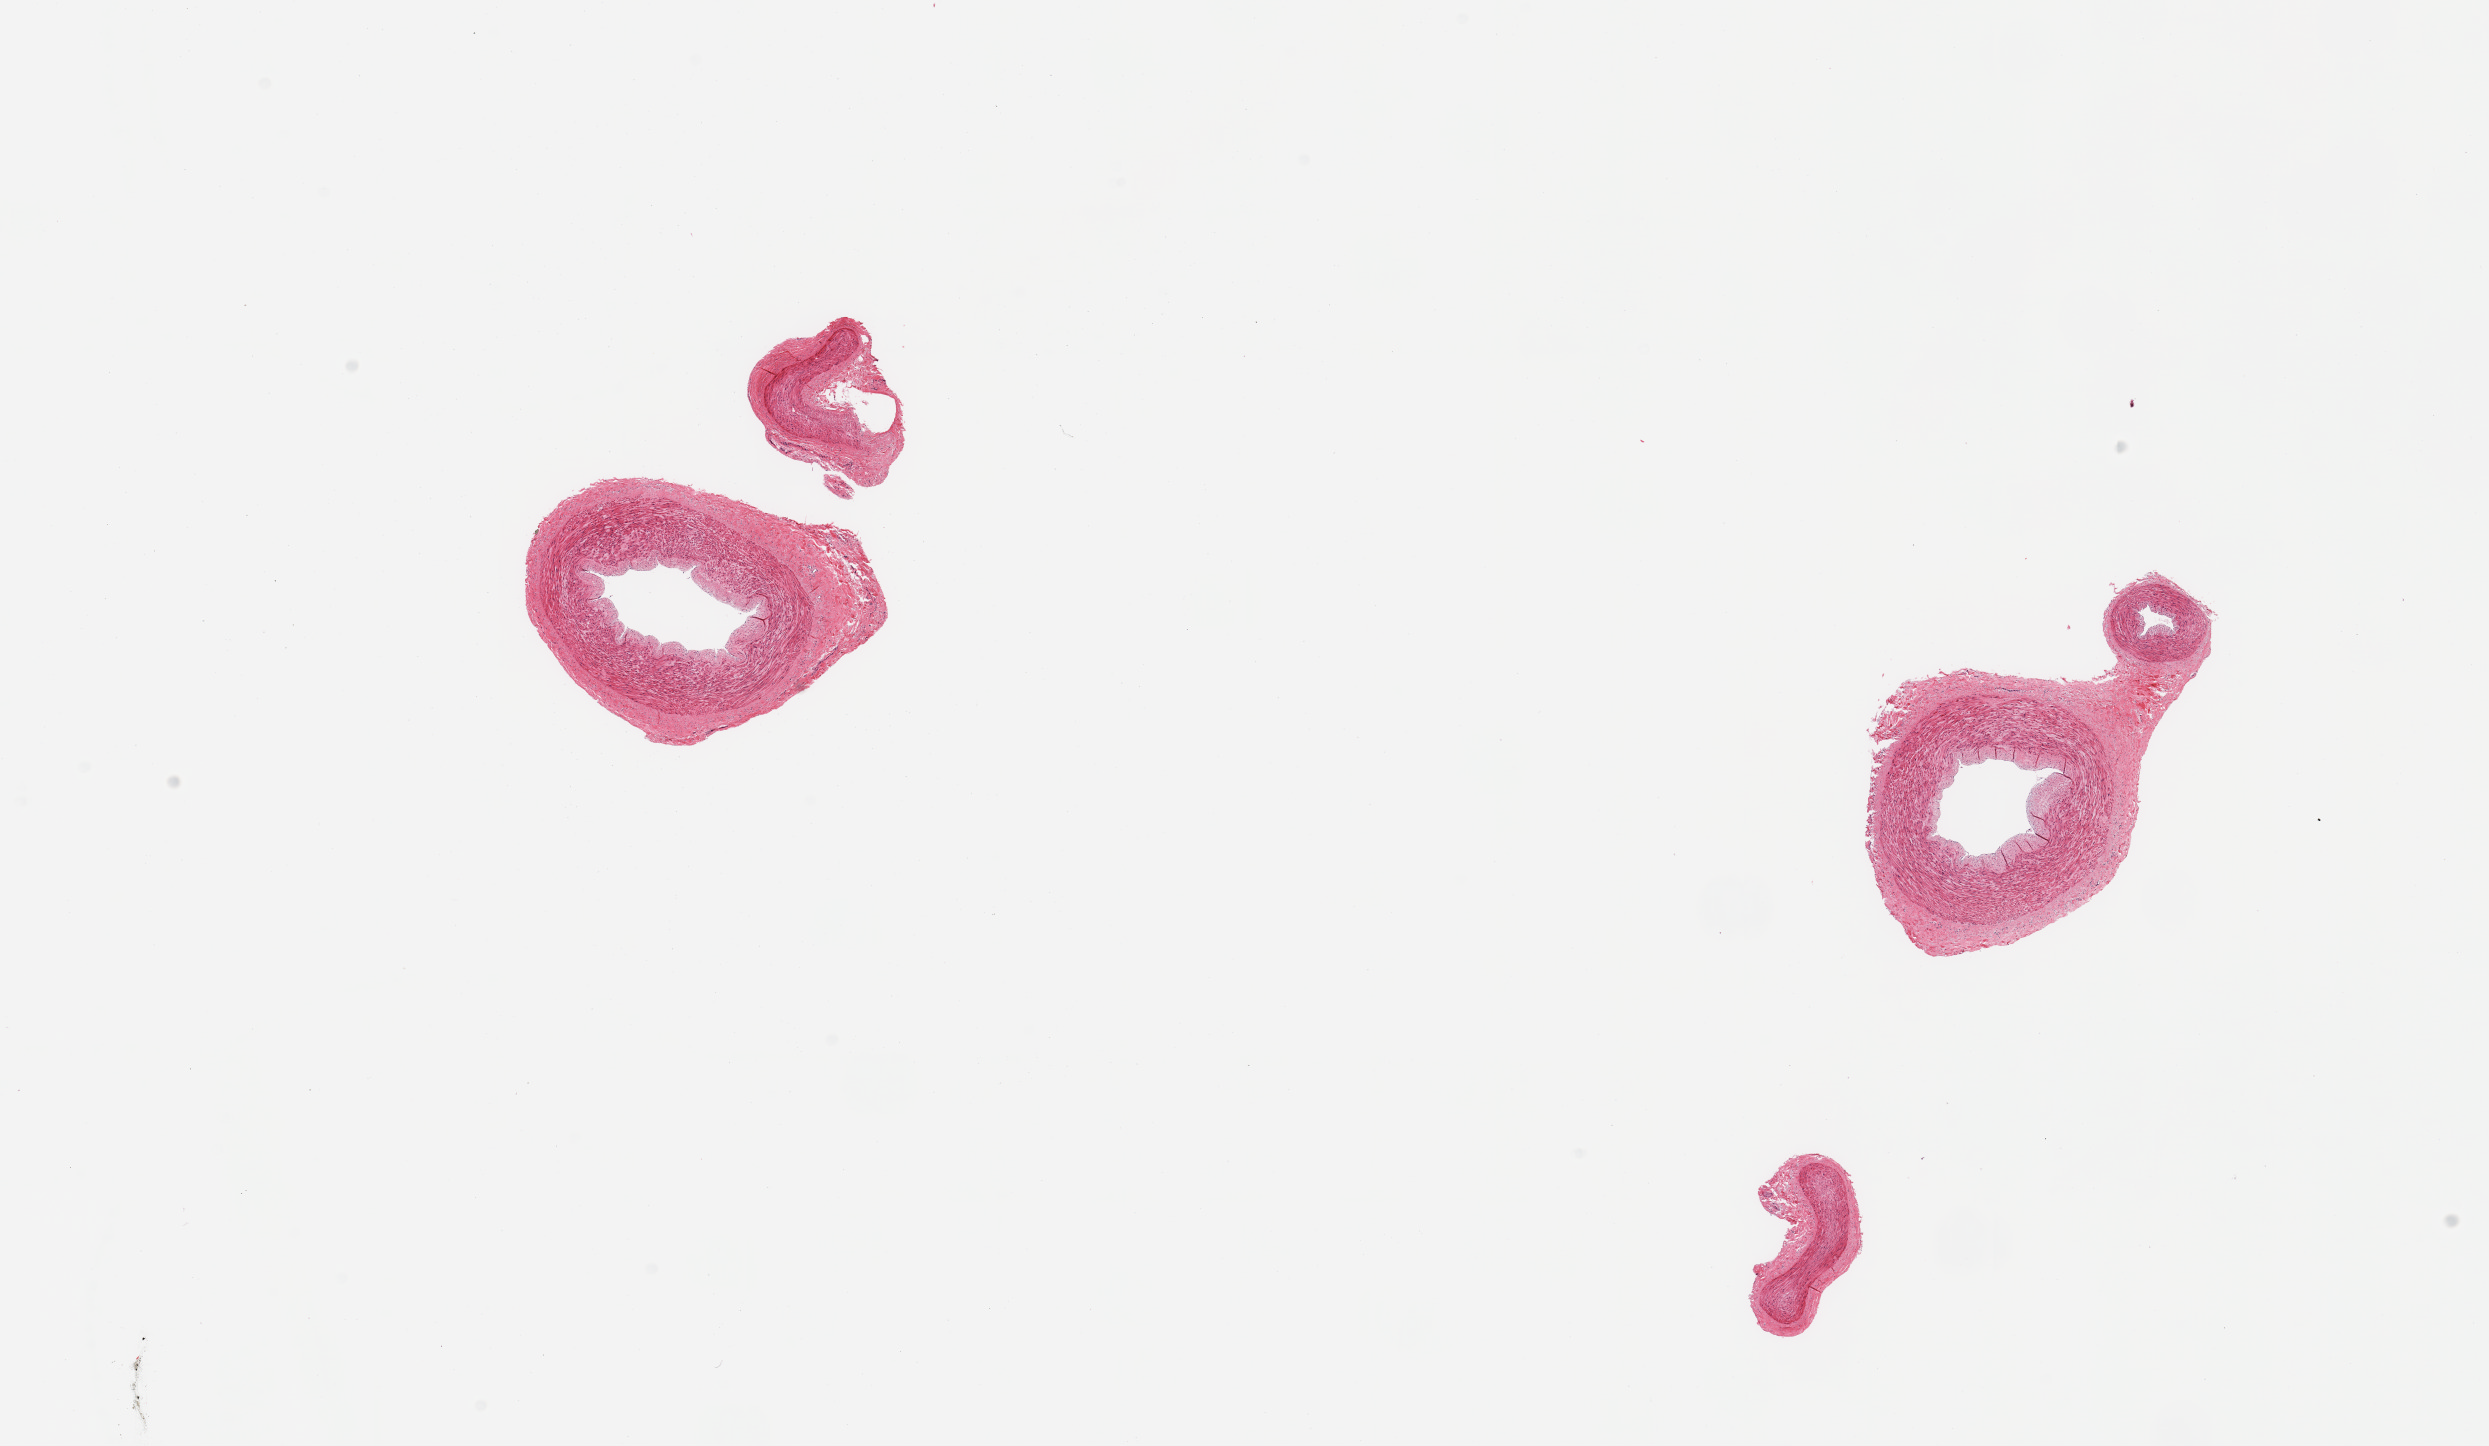
Hematoxylin and eosin (H&E) whole-slide image, shown as a low-resolution overview of the whole scanned area (about 19.7 x 11.4 mm). PAXgene-fixed, paraffin-embedded tissue. Sampled site (target tissue): tibial artery. Tissue donor sample. Female donor.
Reviewer comment on this tissue sample: 2 pieces small muscular artery, adherent fibrous tissue, smaller vessel up to ~0.4mm.